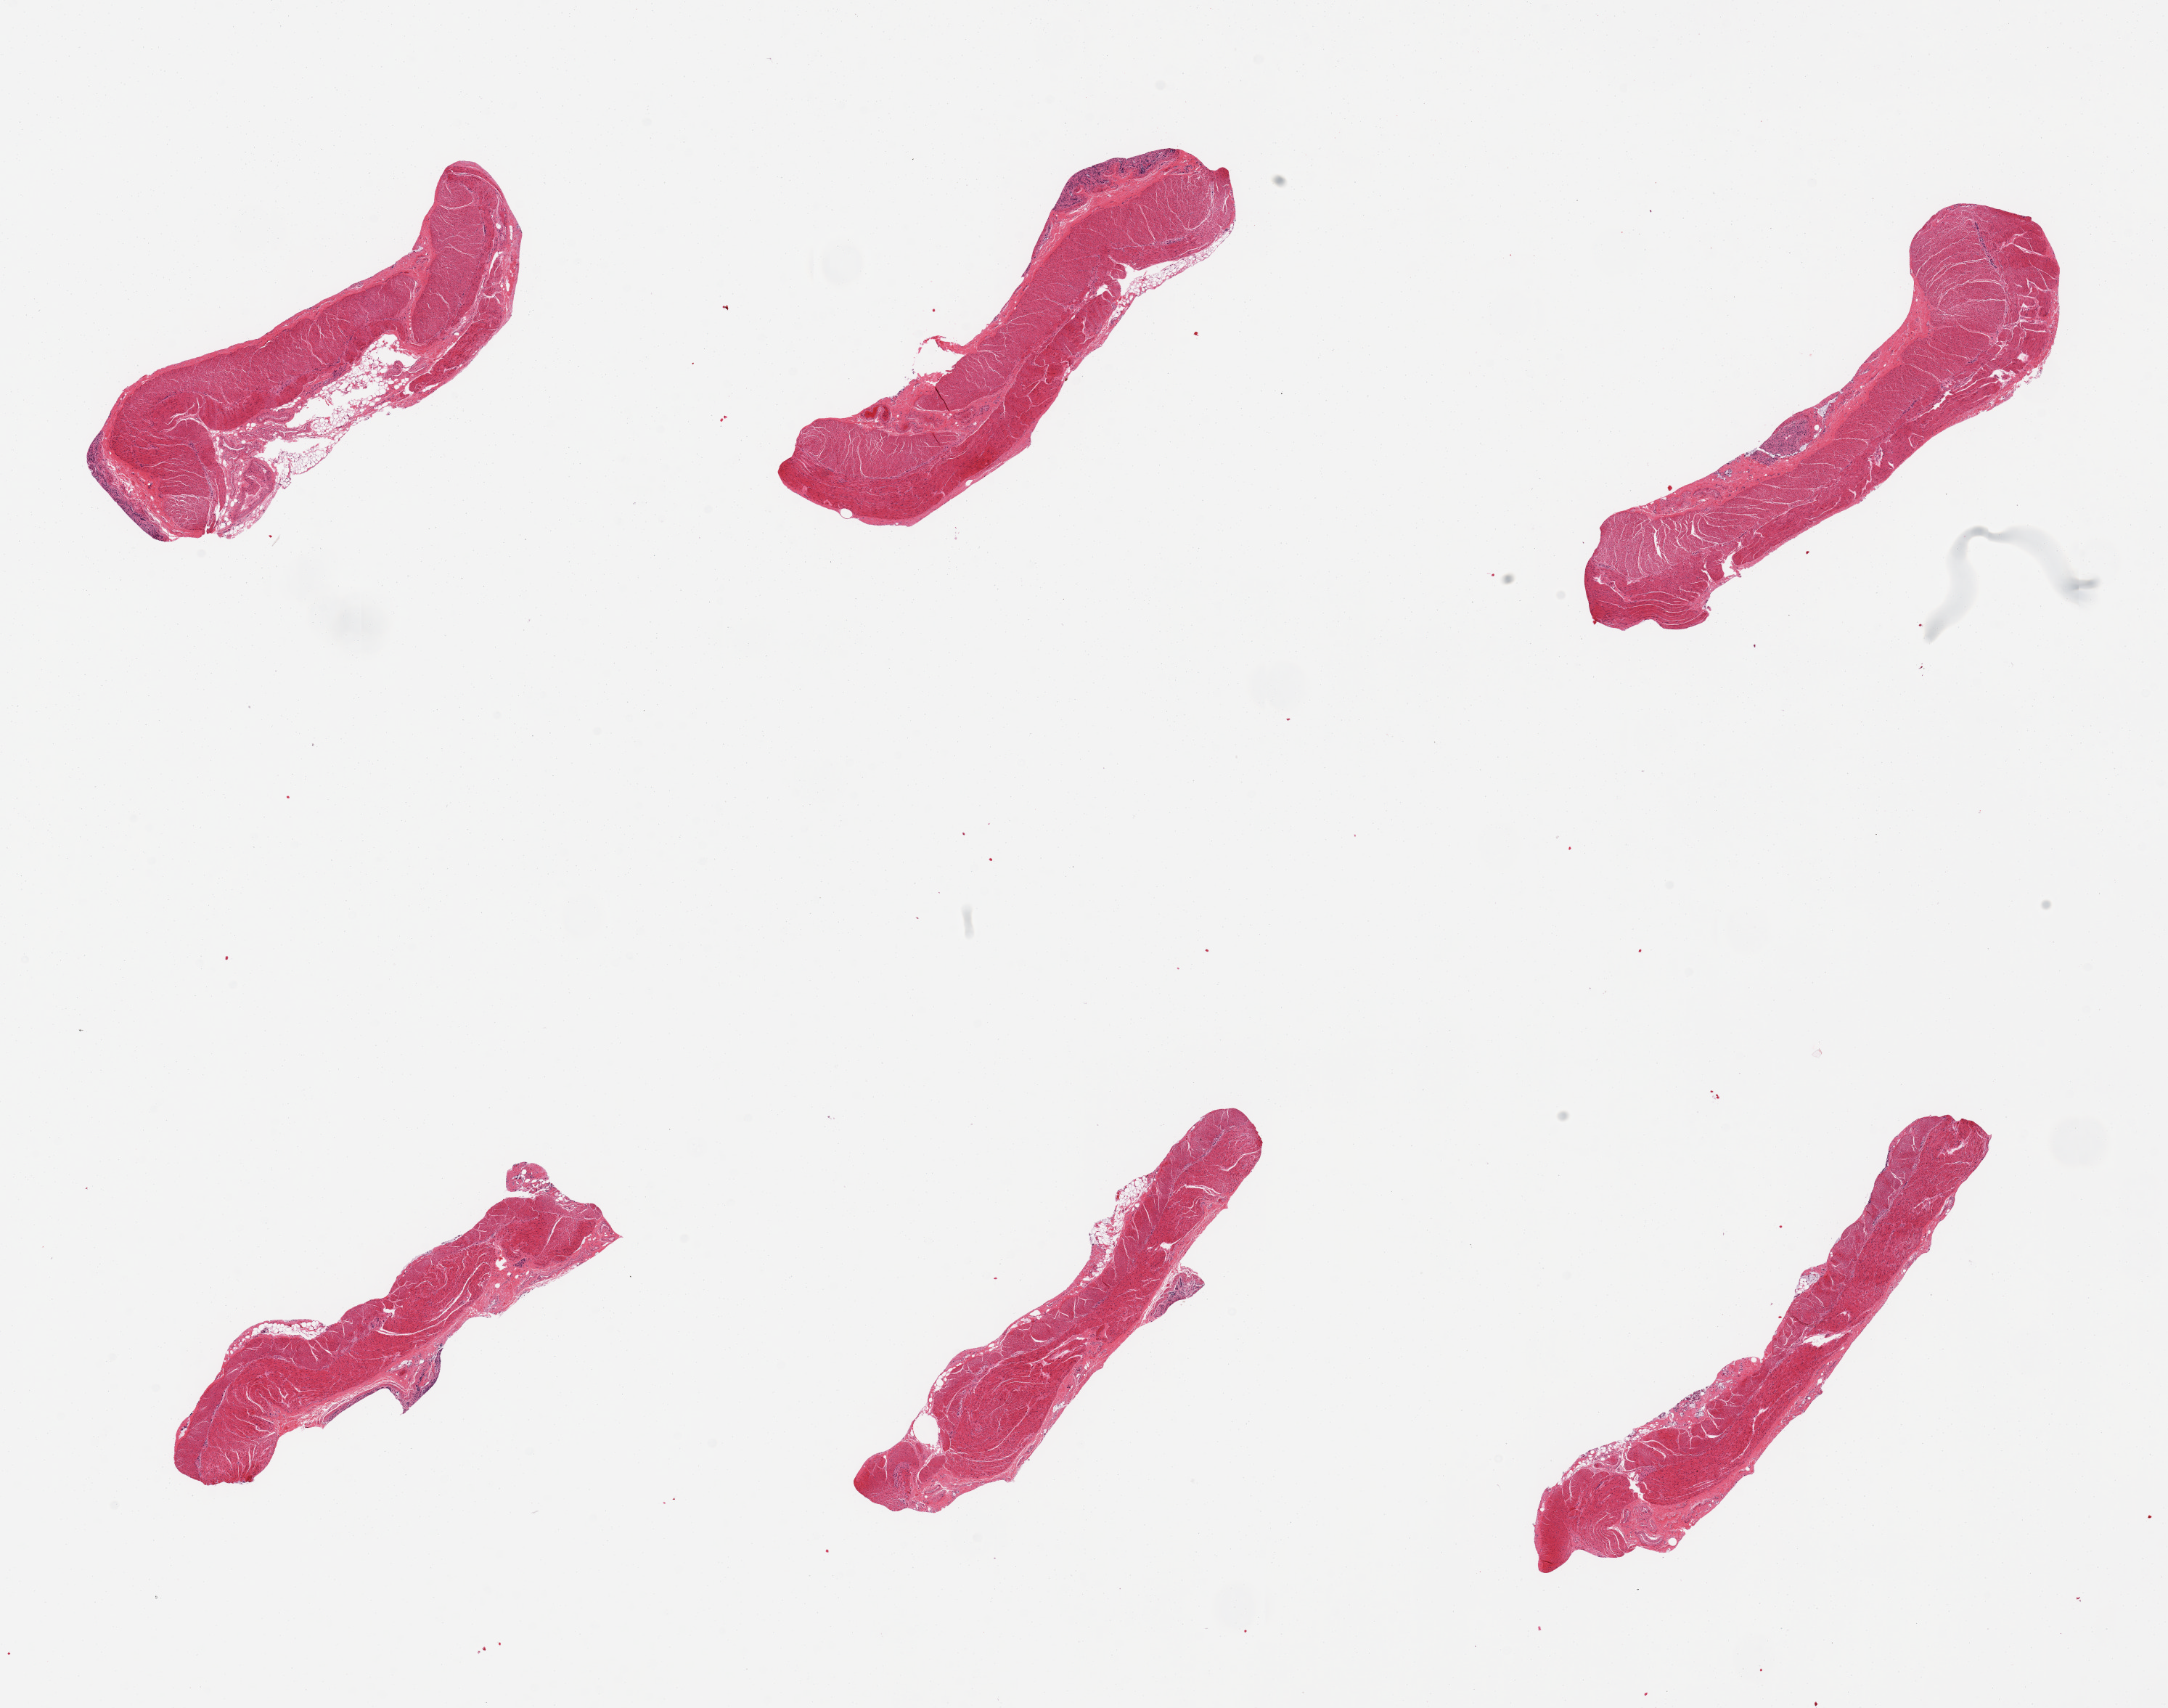
H&E whole-slide image, low-resolution overview of the scanned area, about 23.6 x 18.6 mm. PAXgene-fixed, paraffin-embedded tissue. Sampled site (target tissue): sigmoid colon. Donor tissue sample.
• pathologist's review note for this sample: 6 pieces; small amounts of totally autolyzed mucosa; muscle slightly autolyzed